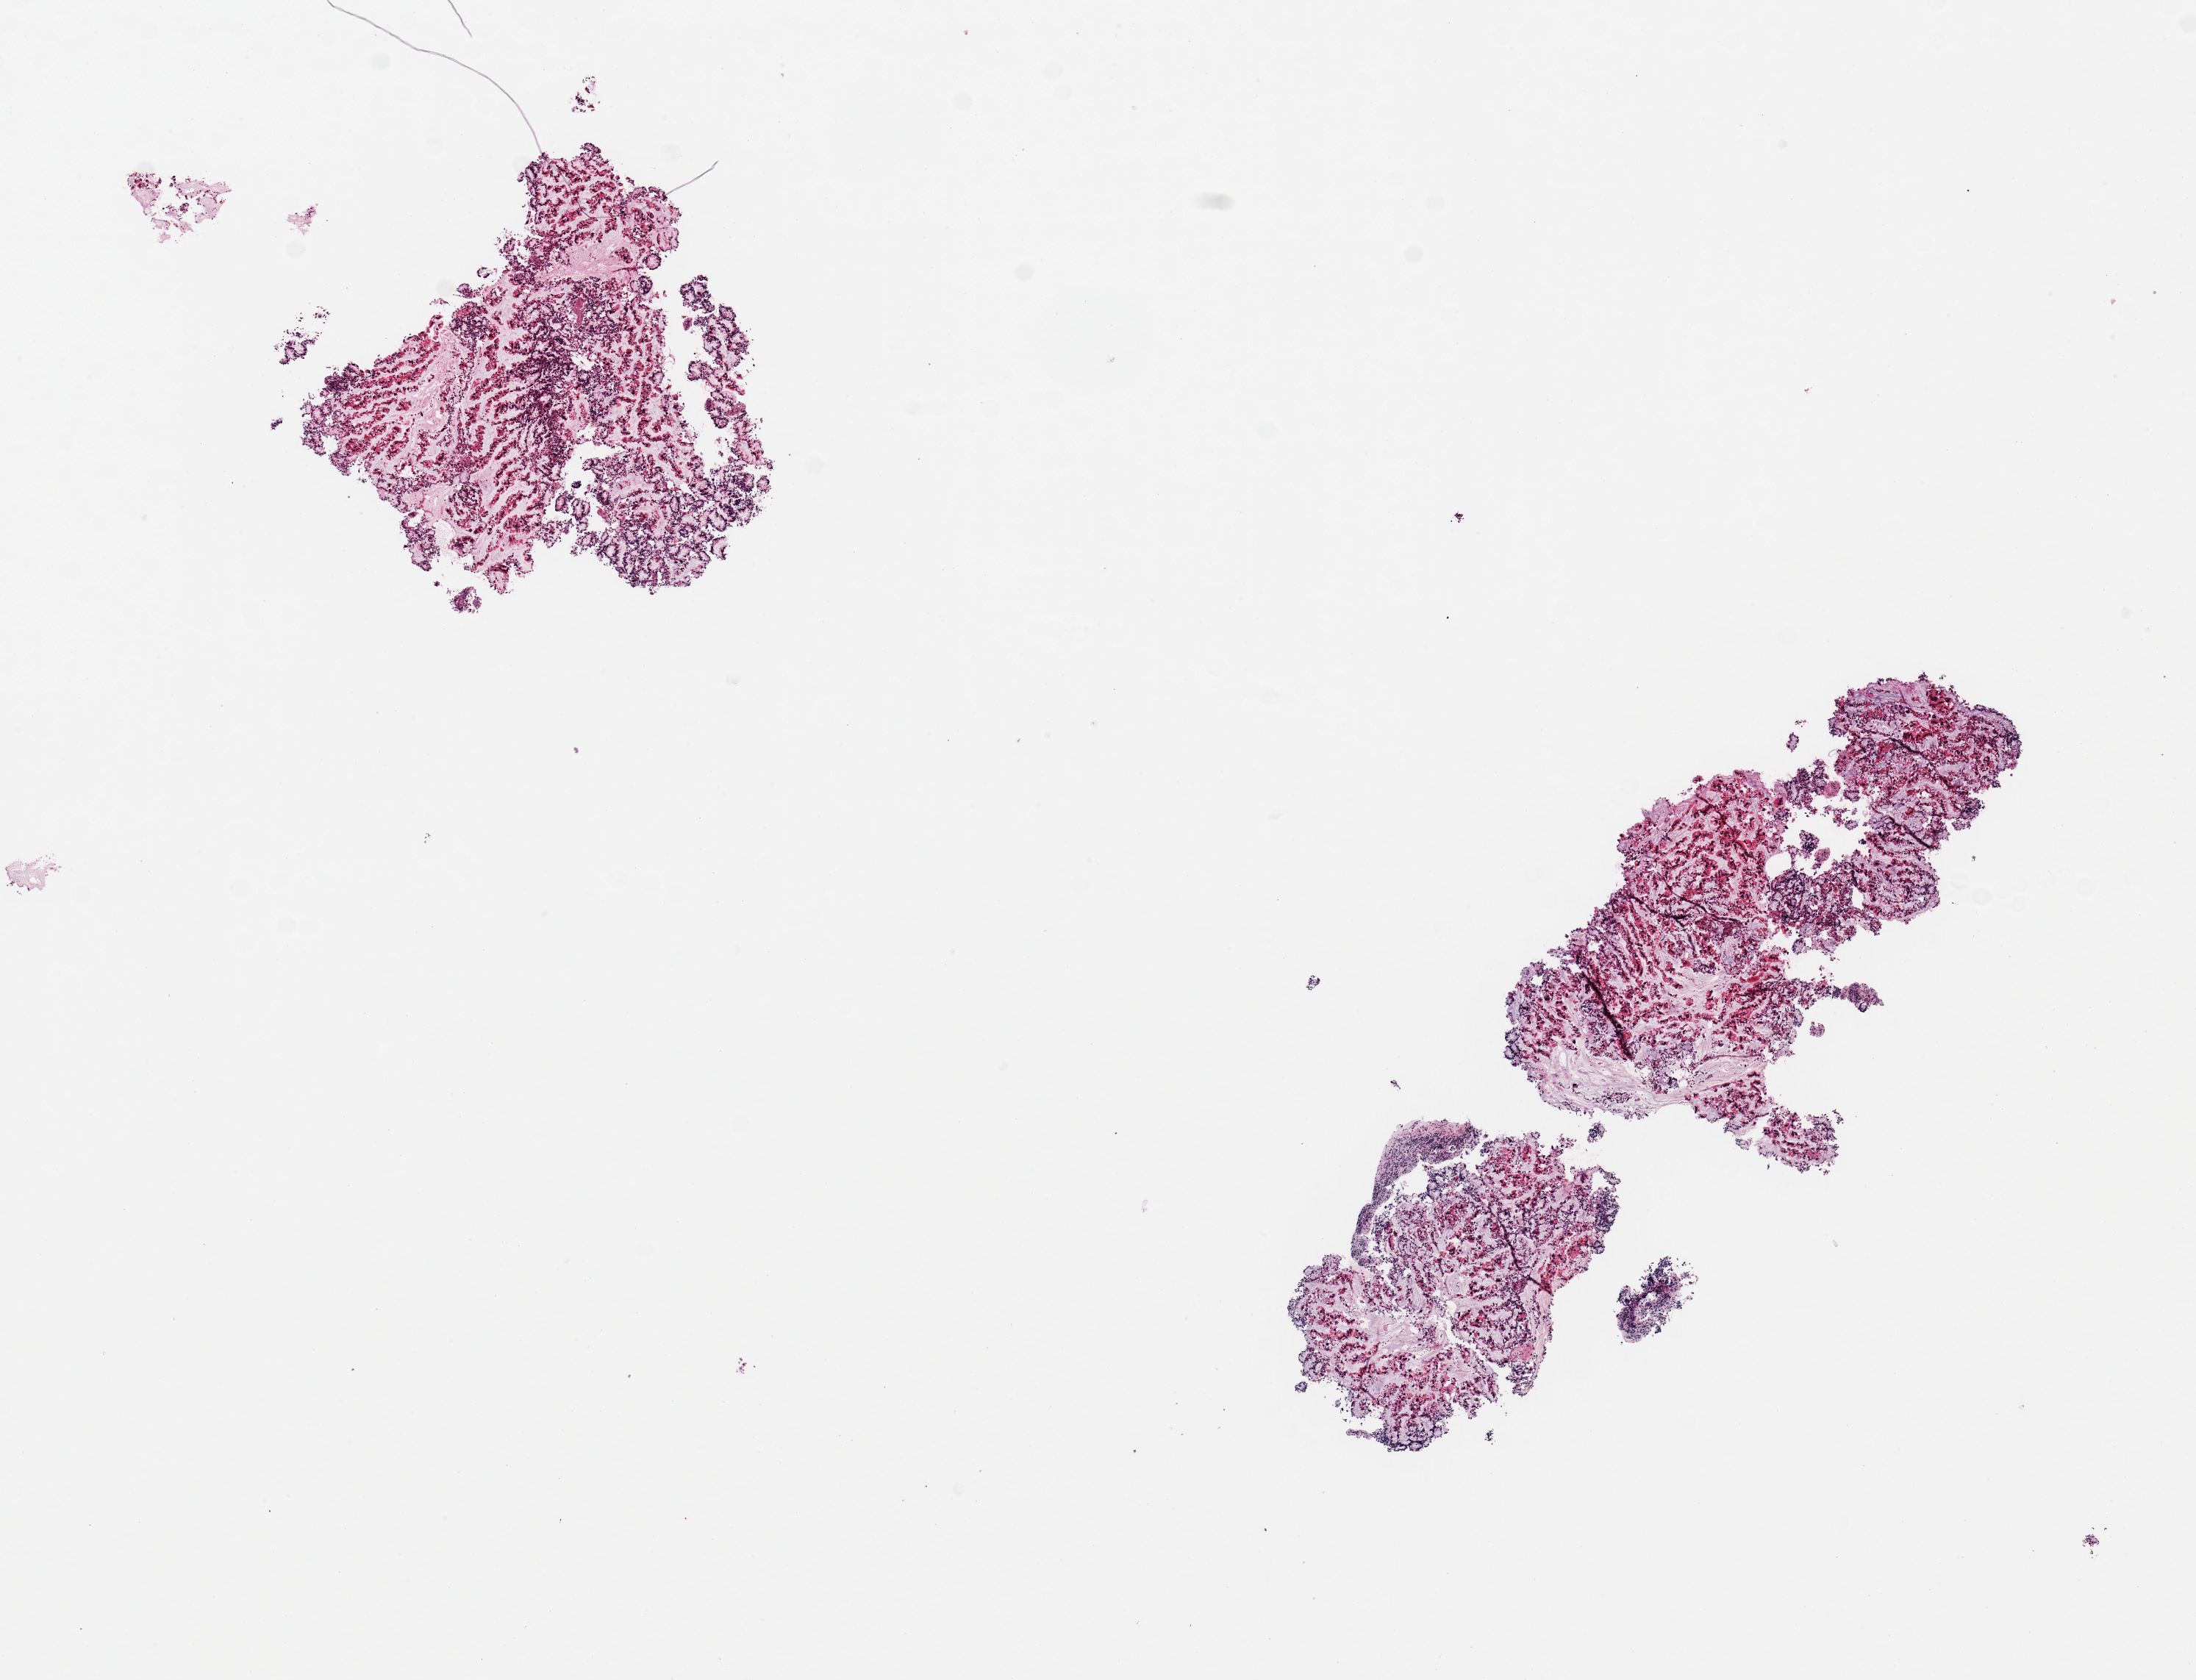
Digitized hematoxylin and eosin (H&E)-stained section, brightfield, whole scanned area (about 11.8 x 9.0 mm, acquisition: 20x scan) shown as a low-resolution overview. PAXgene-fixed paraffin-embedded (PFPE) section. Section of ileum (target tissue). Tissue donor sample. Male donor.
Reviewer comment on this tissue sample: 2 piece 4x2mm, all mucosa, no lymphoid tissue, badly autolyzed.